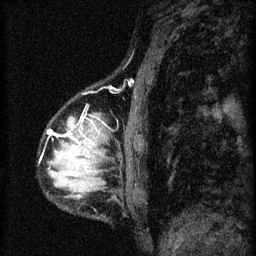
Breast MRI (dynamic contrast-enhanced), one sagittal slice. Position 12 of 60 along the scan axis. 3 images stored at this slice position (order not interpretable as contrast timing). 1.5 T. TE 4.2 ms, TR 8.2 ms. 2 mm slice thickness. 256 × 256 image matrix, field of view 180 × 180 mm. Female patient, age 37 years.
Annotated regions visible in this slice (semi-automatically segmented with operator editing):
- analysis volume of interest (the breast-tissue region the enhancement analysis was run in; not a lesion): bounding box (x1, y1, x2, y2) in pixels: (49, 114, 113, 197)
- tumour enhancement mask (voxels above the 70 % enhancement threshold inside the analysis volume of interest): (53, 132, 95, 145)